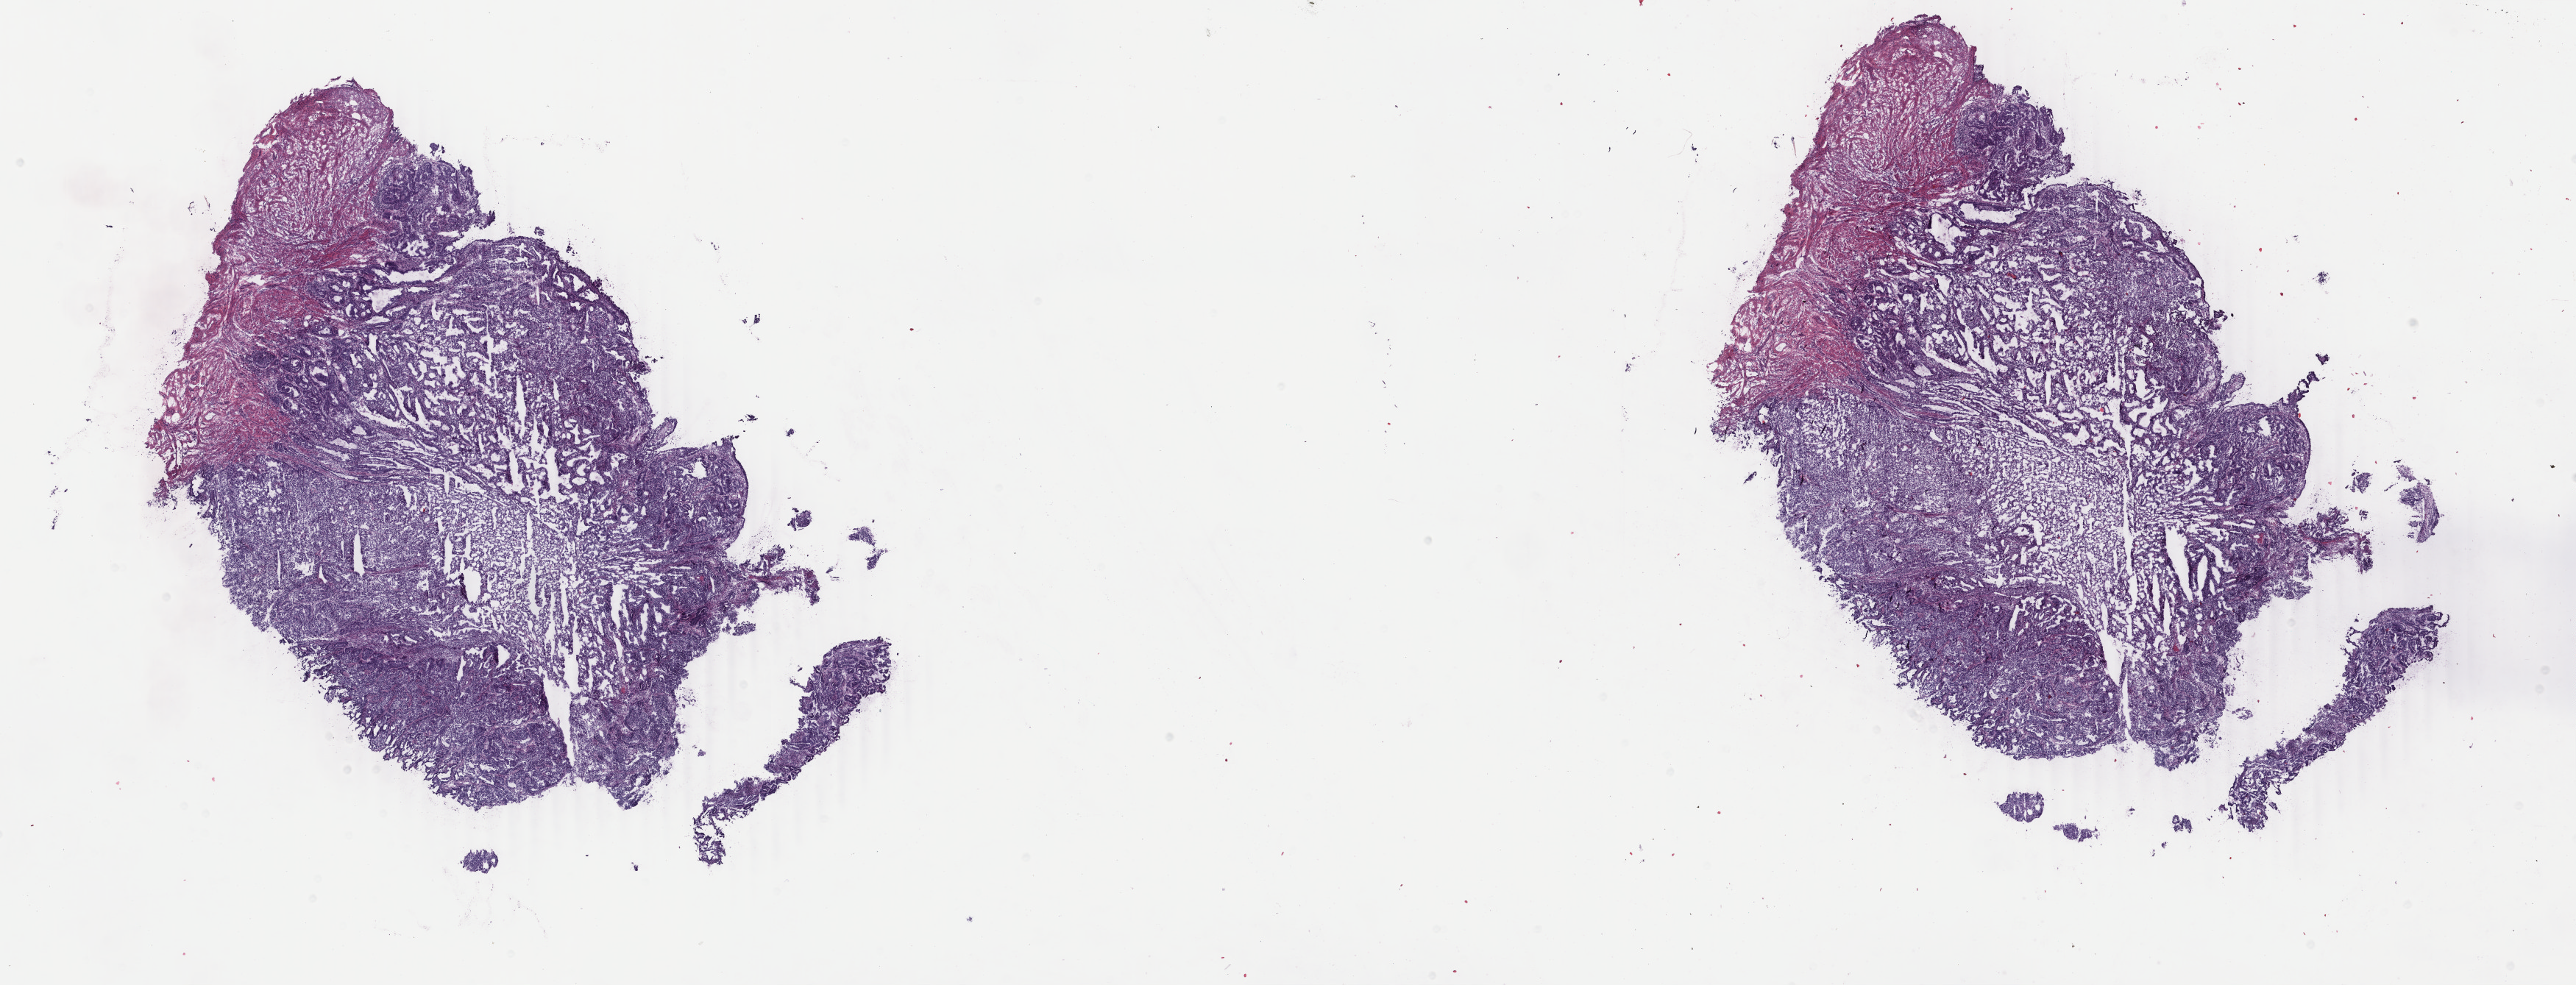
Whole-slide histology image, H&E — low-resolution overview of the scanned area, about 27.8 x 10.6 mm; frozen section; uterus, primary tumour sample. Patient: female, age at initial diagnosis 33 years. Histologic grade: G3 (poorly differentiated). Pathologist review of this section (percent, as recorded): tumour cells 85%, tumour nuclei 65%, normal cells 15%, stromal cells 0%, necrosis 0%. Infiltration values recorded for this section: lymphocyte infiltration 0%, monocyte infiltration 0%, neutrophil infiltration 0%.
FIGO stage: IIIC2. Pathologic diagnosis: Endometrioid adenocarcinoma, NOS (endometrium).